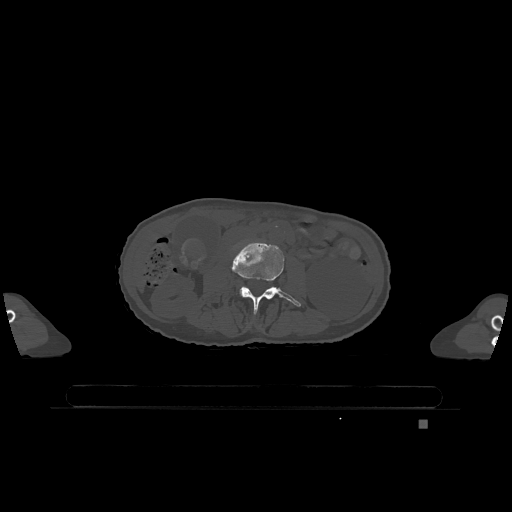
CT including the spine, one axial slice. Position 352 of 1317 along the scan axis. Bone window (W 1800 / L 400 HU). 0.5 mm slice thickness. 512 × 512 image matrix, field of view 500 × 500 mm. Female patient, age 74 years. From the clinical record (not read from this slice): primary cancer: lung.
Outlined on this slice (semi-automatically segmented with operator editing):
- L3 vertebra: box from (x=230, y=242) to (x=301, y=314) px